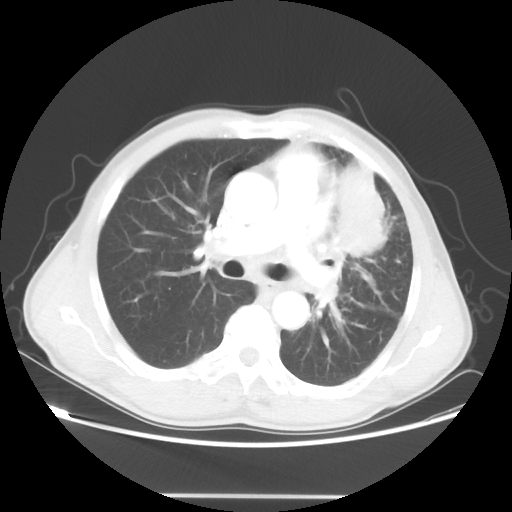
Chest CT, one axial slice. Position 31 of 55 along the scan axis. 100 kVp. Lung window (W 1500 / L -600 HU). 512 × 512 image matrix, field of view 398 × 398 mm. Patient: male, 60 years. Case-level facts recorded for this patient, not image findings: clinical TNM (as recorded): T3 N3 M0.
Outlined on this slice (rectangle marked by the reading radiologist):
- lung tumour (recorded histology: adenocarcinoma): box from (x=334, y=163) to (x=389, y=263) px